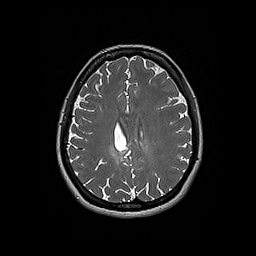
Brain MRI from a brain-tumour surgery series, one axial slice; slice 71 of 192 in the series (ordered by position); 1 mm slice thickness; 256 × 256 image matrix. From the clinical record (not read from this slice): histopathology: Oligodendroglioma; WHO grade: 2; IDH mutation: yes.
Structures marked on this image (outlined manually by an expert reader):
- tumour: bounding box (x1, y1, x2, y2) in pixels: (109, 146, 124, 163)